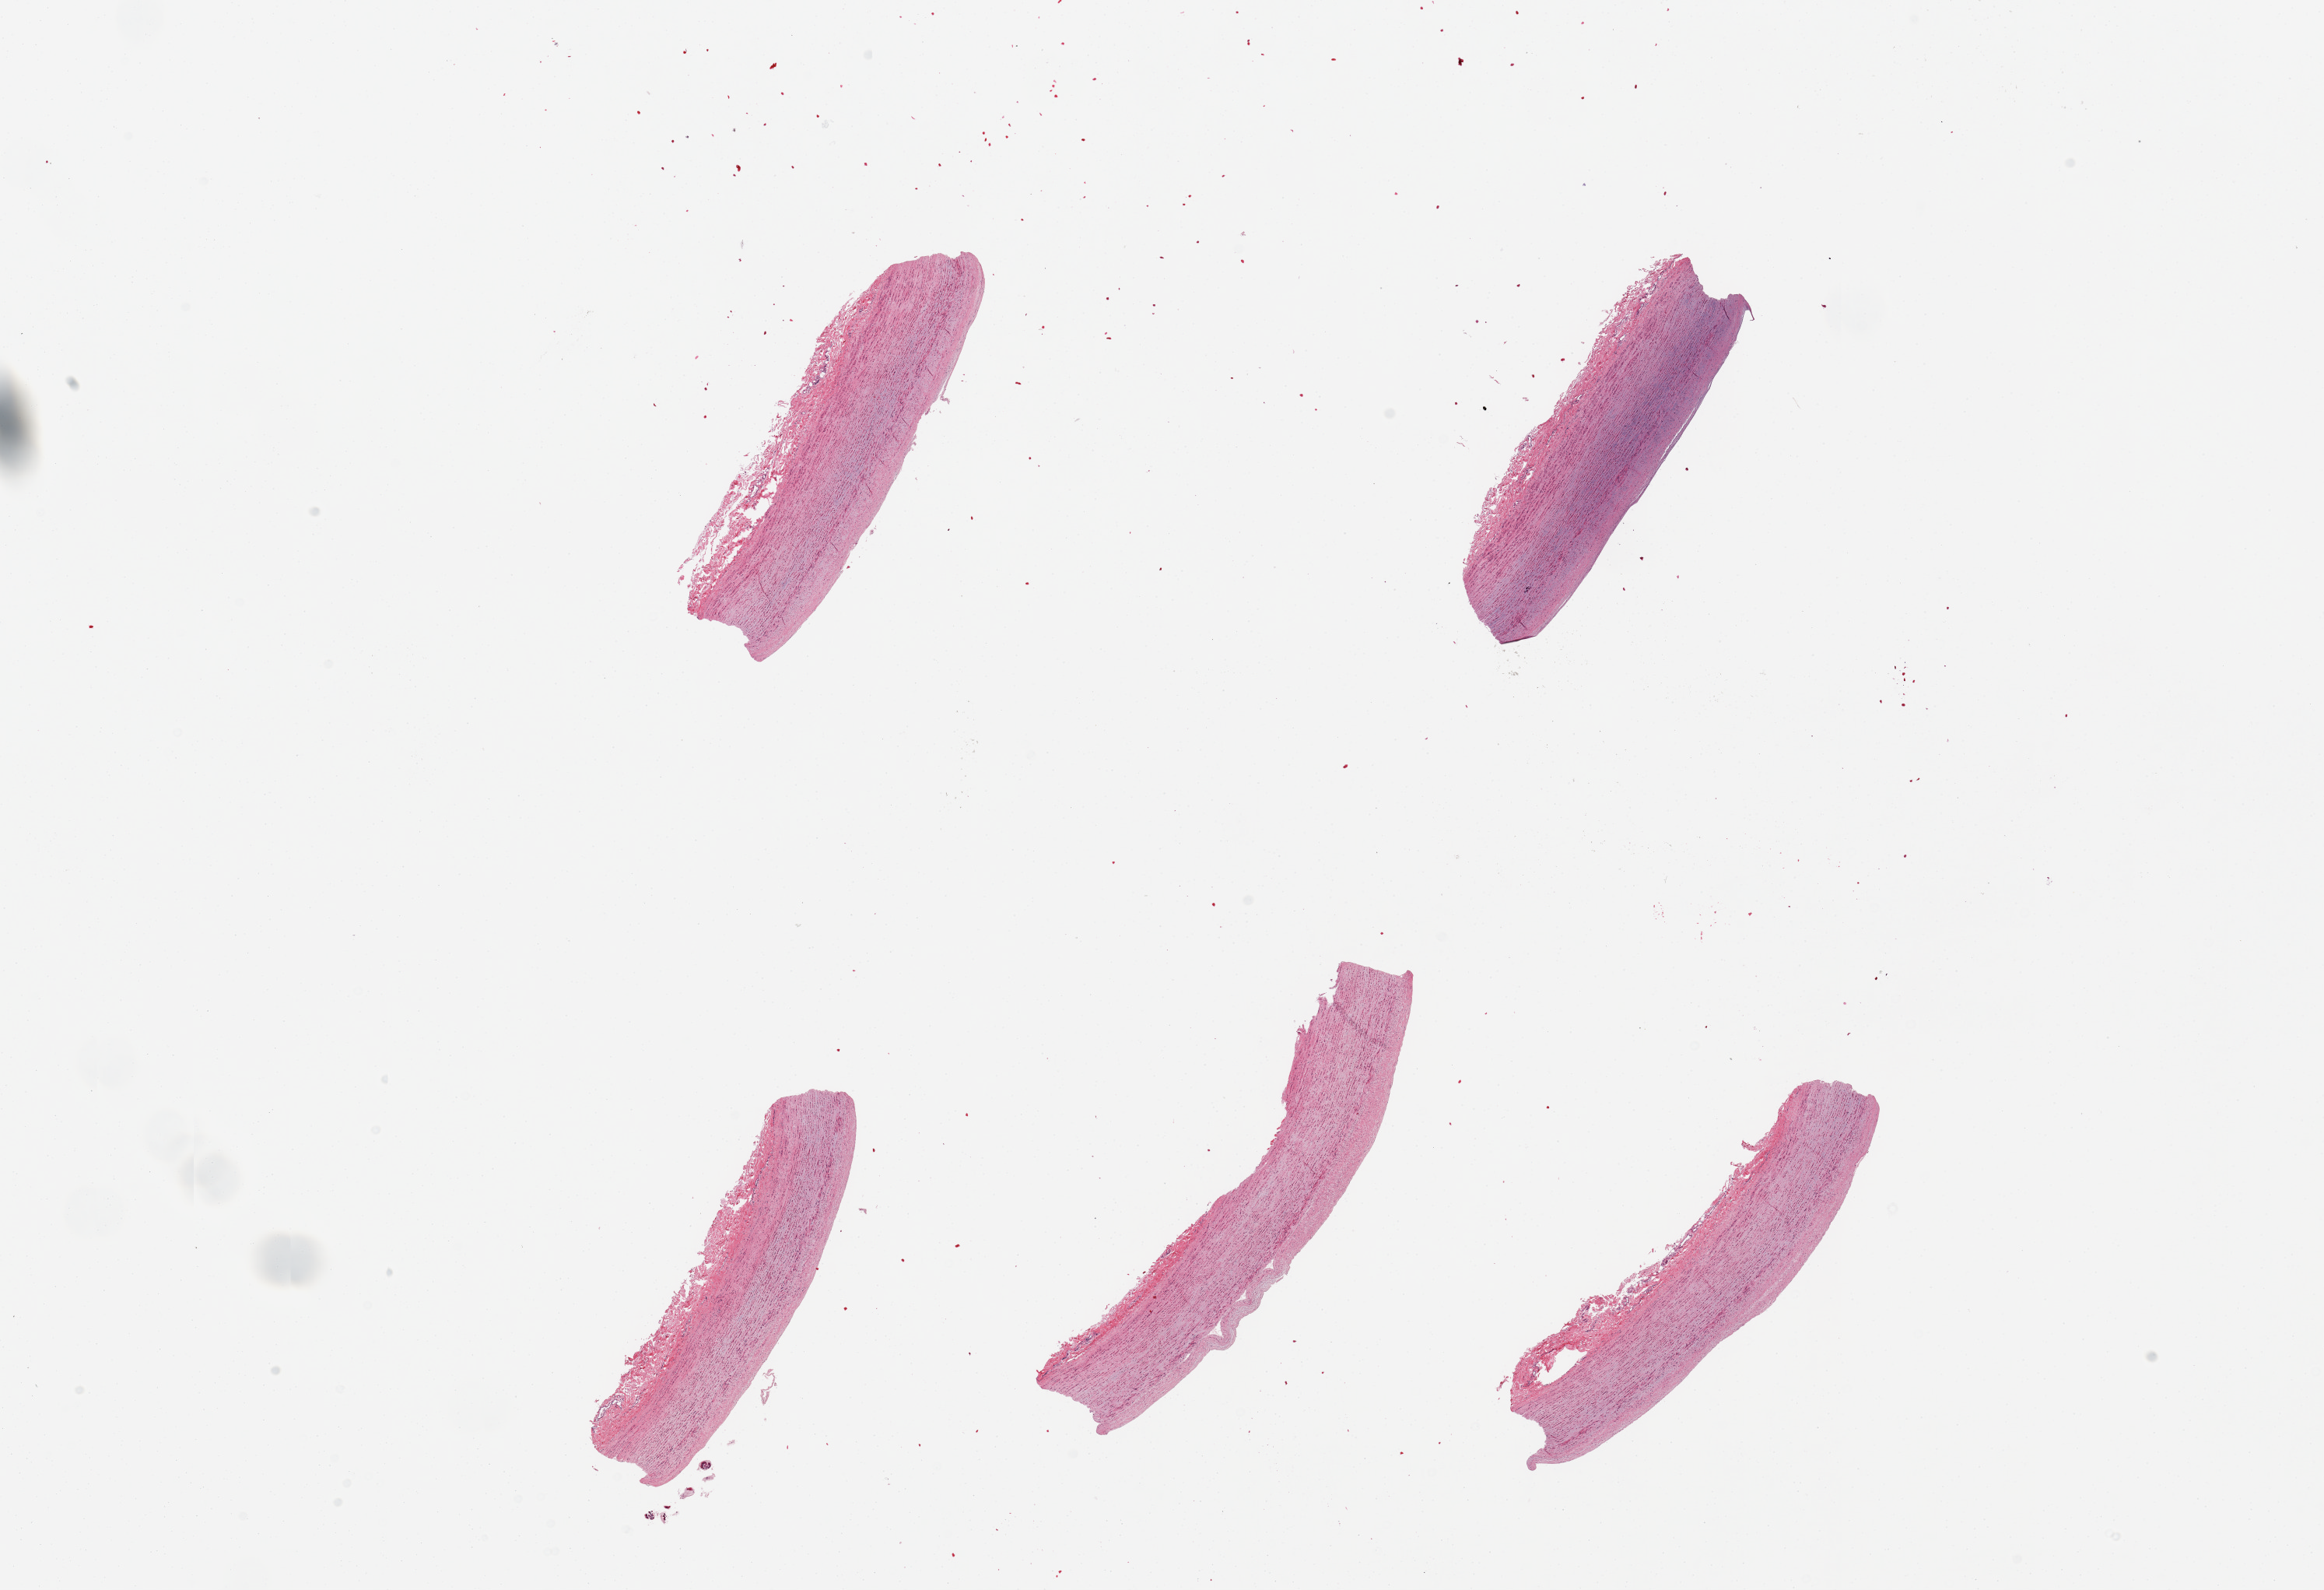
Whole-slide image, hematoxylin and eosin (H&E) stain, whole scanned area (about 23.6 x 16.2 mm, from a 20x scan) shown as a low-resolution overview, PAXgene-fixed, paraffin-embedded tissue, target tissue: aorta, tissue donor sample. Donor: male.
• review note (as recorded): 5 pieces, minimal atherosis